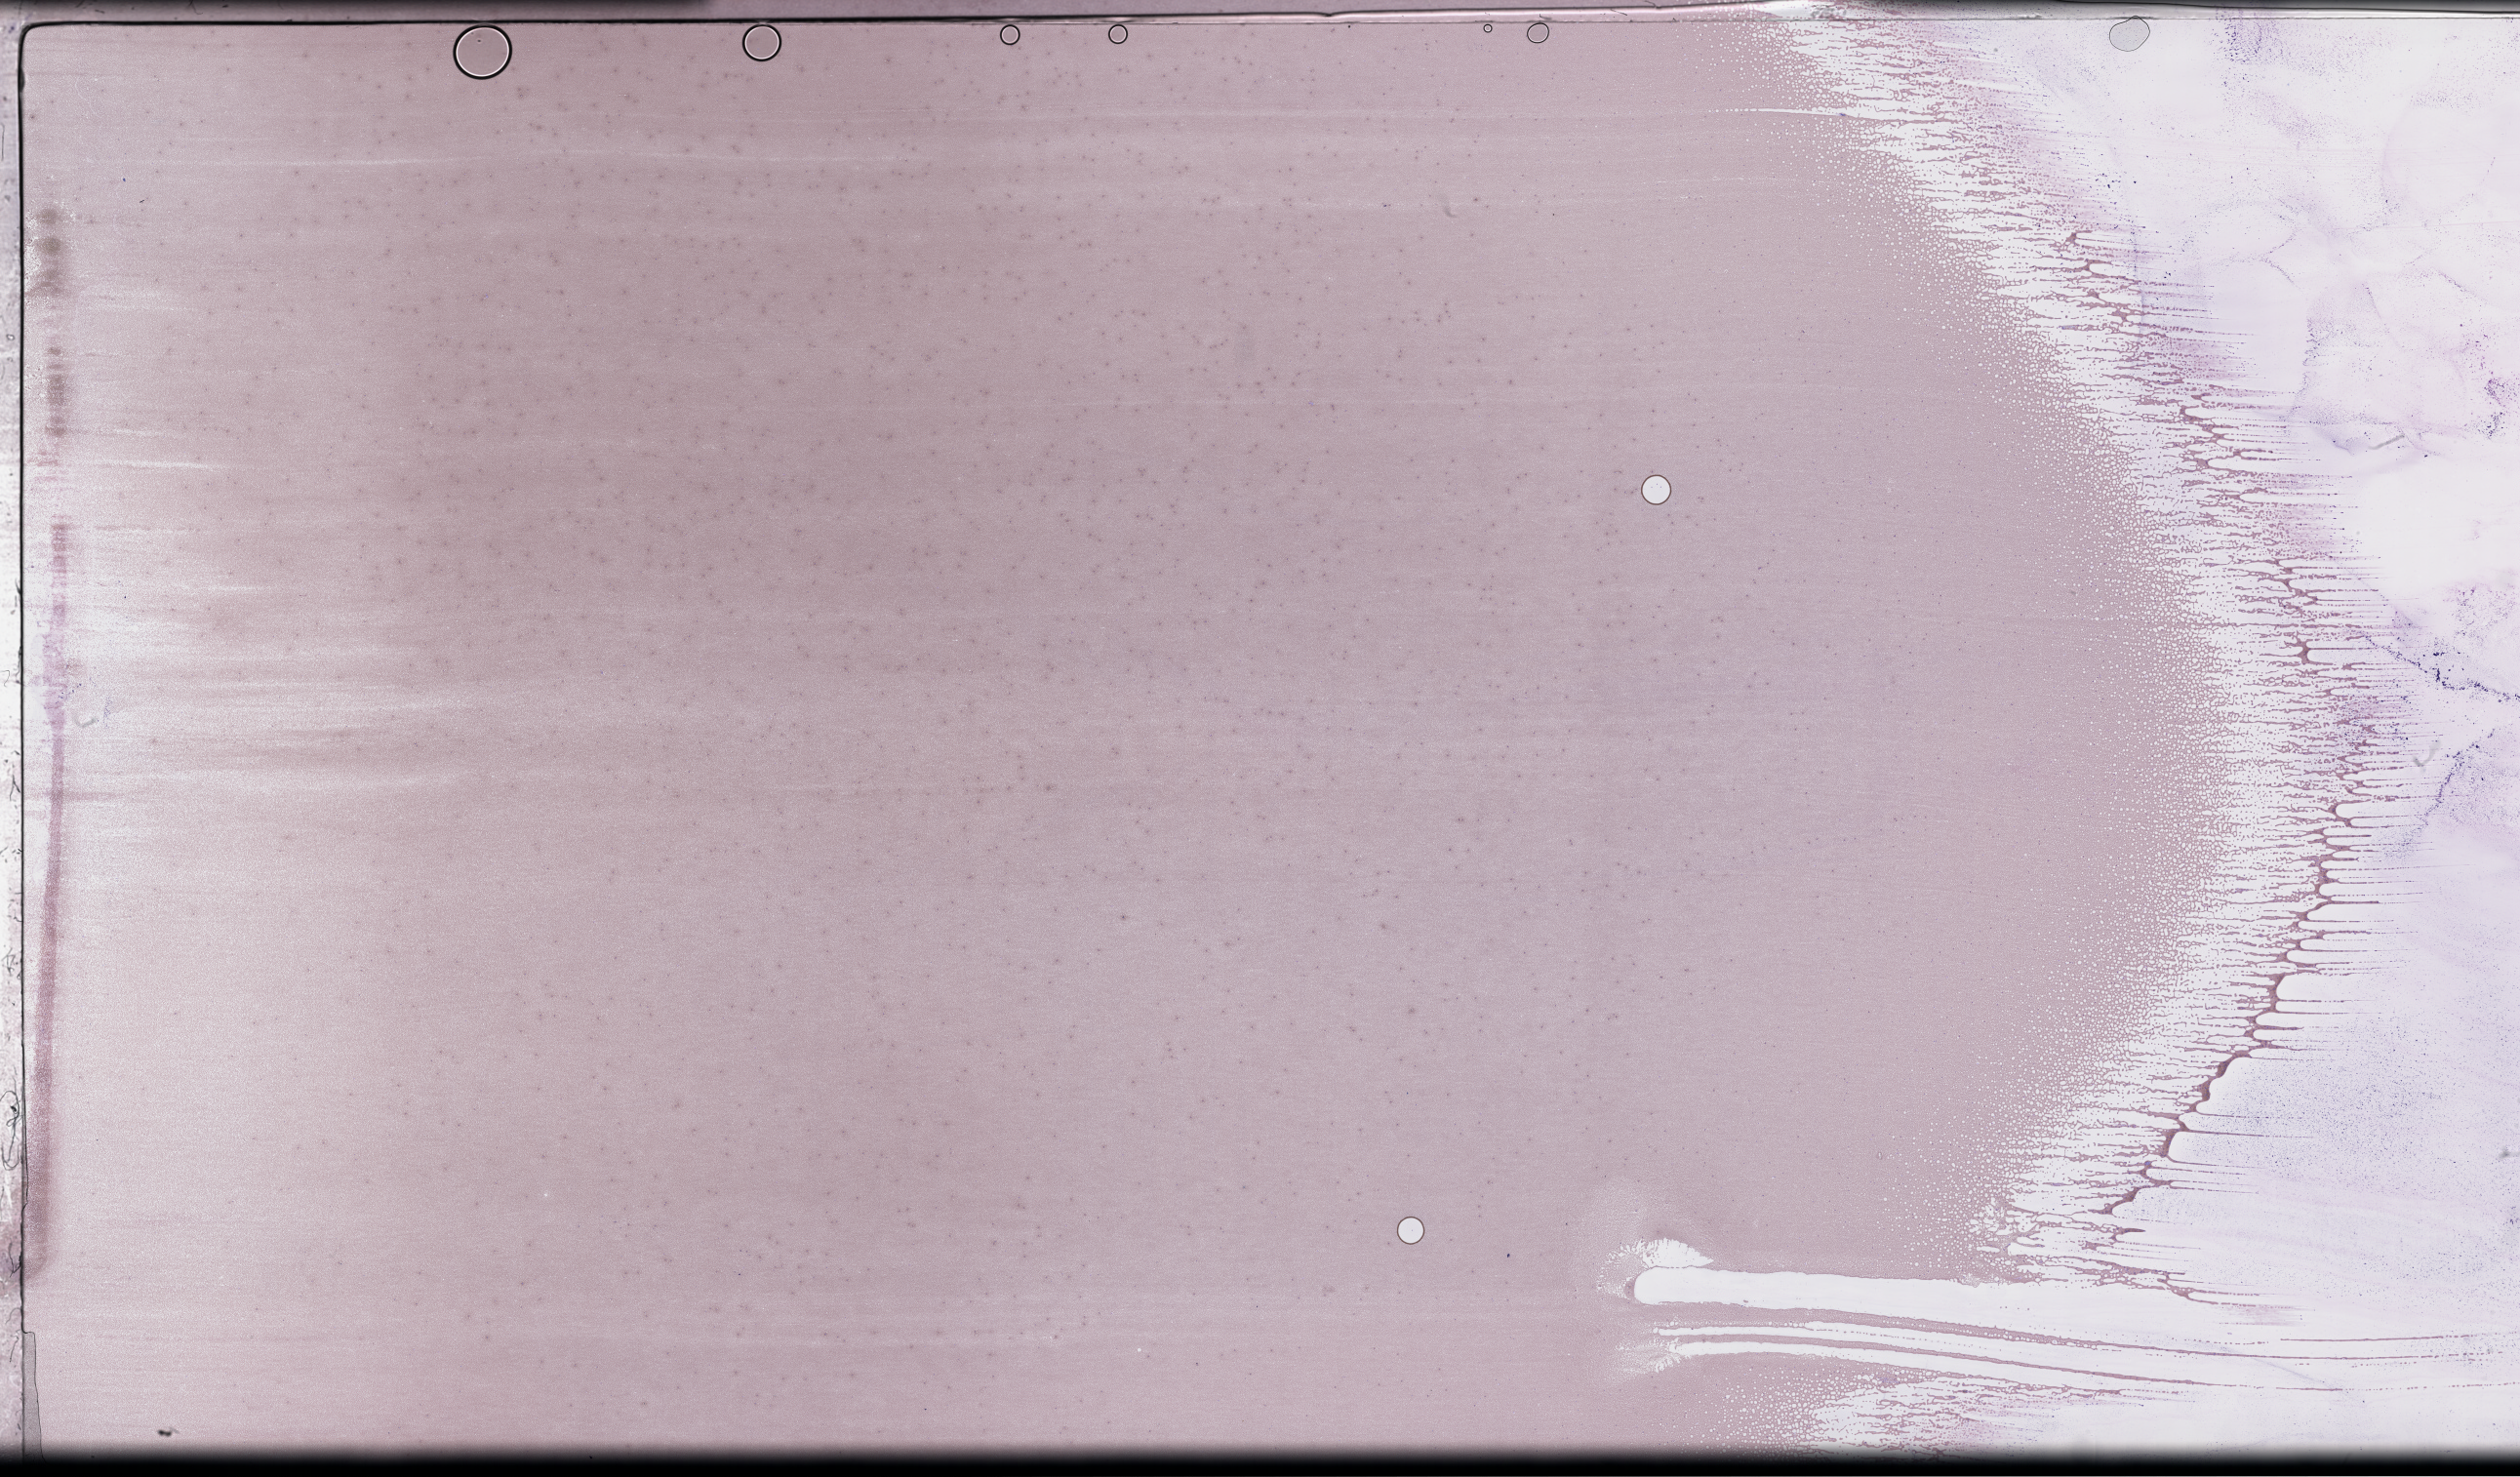
Wright–Giemsa-stained whole blood smear, whole-slide image, shown as a low-resolution overview of the whole scanned area (about 41.7 x 24.5 mm); EDTA-anticoagulated smear; specimen time point: collected on treatment. Patient sex: male.
Patient diagnosis: Plasma Cell Myeloma.